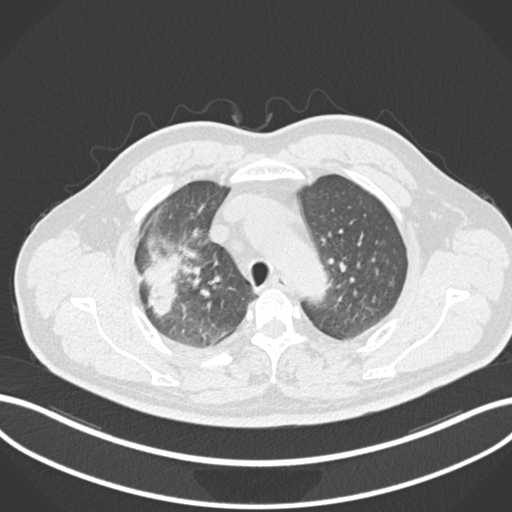
Chest CT, one axial slice; reconstruction kernel B30f; 120 kVp; lung window (W 1500 / L -600 HU); 1 mm slice thickness; 512 × 512 image matrix, field of view 400 × 400 mm. Patient: male, 55 years. From the clinical record (not read from this slice): clinical TNM (as recorded): T3 N2 M1.
Annotated regions visible in this slice (bounding box drawn by a radiologist):
- lung tumour (recorded histology: adenocarcinoma): bounding box [x1, y1, x2, y2] px = [142, 241, 183, 321]